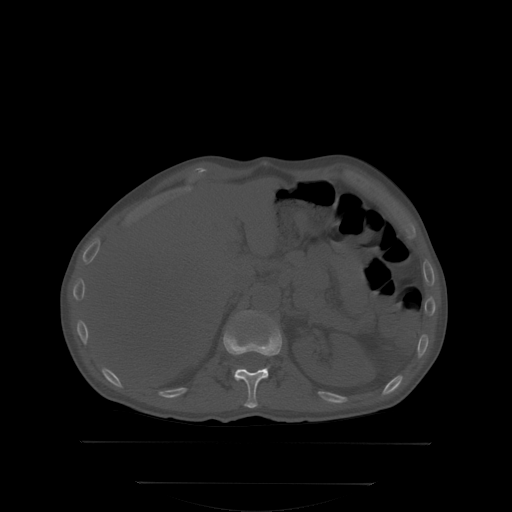
CT including the spine, one axial slice; slice 164 of 350 in the series (ordered by position); bone window (W 1800 / L 400 HU); 2.5 mm slice thickness; 512 × 512 image matrix, field of view 500 × 500 mm. Patient: male, 58 years. From the clinical record (not read from this slice): primary cancer: prostate; vertebrae with lytic lesions (as recorded): L1.
Outlined on this slice (semi-automatically segmented with operator editing):
- L1 vertebra: bounding box (x1, y1, x2, y2) in pixels: (232, 311, 269, 373)
- T12 vertebra: (223, 320, 282, 408)